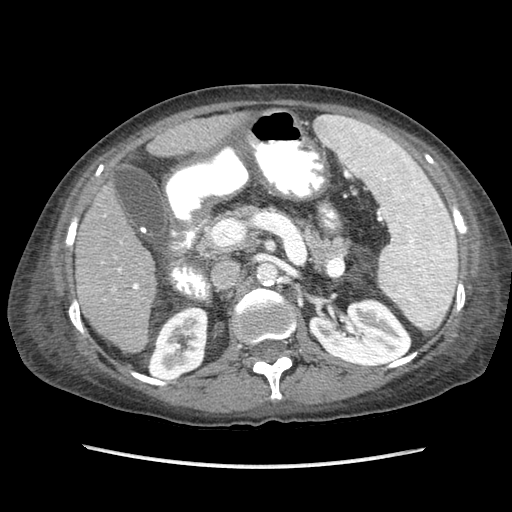
Contrast-enhanced abdominal CT (liver protocol), one axial slice. Position 36 of 87 along the scan axis. Reconstruction kernel STANDARD. 120 kVp. Soft-tissue window (W 400 / L 40 HU). 2.5 mm slice thickness. 512 × 512 image matrix, field of view 340 × 340 mm. From the clinical record (not read from this slice): diagnosis: hepatocellular carcinoma (patient treated with transarterial chemoembolisation; whether this scan precedes or follows treatment is not stated here); TNM stage (as recorded): Stage-IIIB; Child-Pugh class: A; tumour differentiation: no biopsy; tumour nodularity: uninodular.
Outlined on this slice (semi-automatically segmented with operator editing):
- liver parenchyma outside the tumour (the mass and vessels are separate outlines, so this box may not span the whole liver): bounding box [x1, y1, x2, y2] px = [76, 112, 250, 352]
- liver vessels: [112, 267, 139, 291]